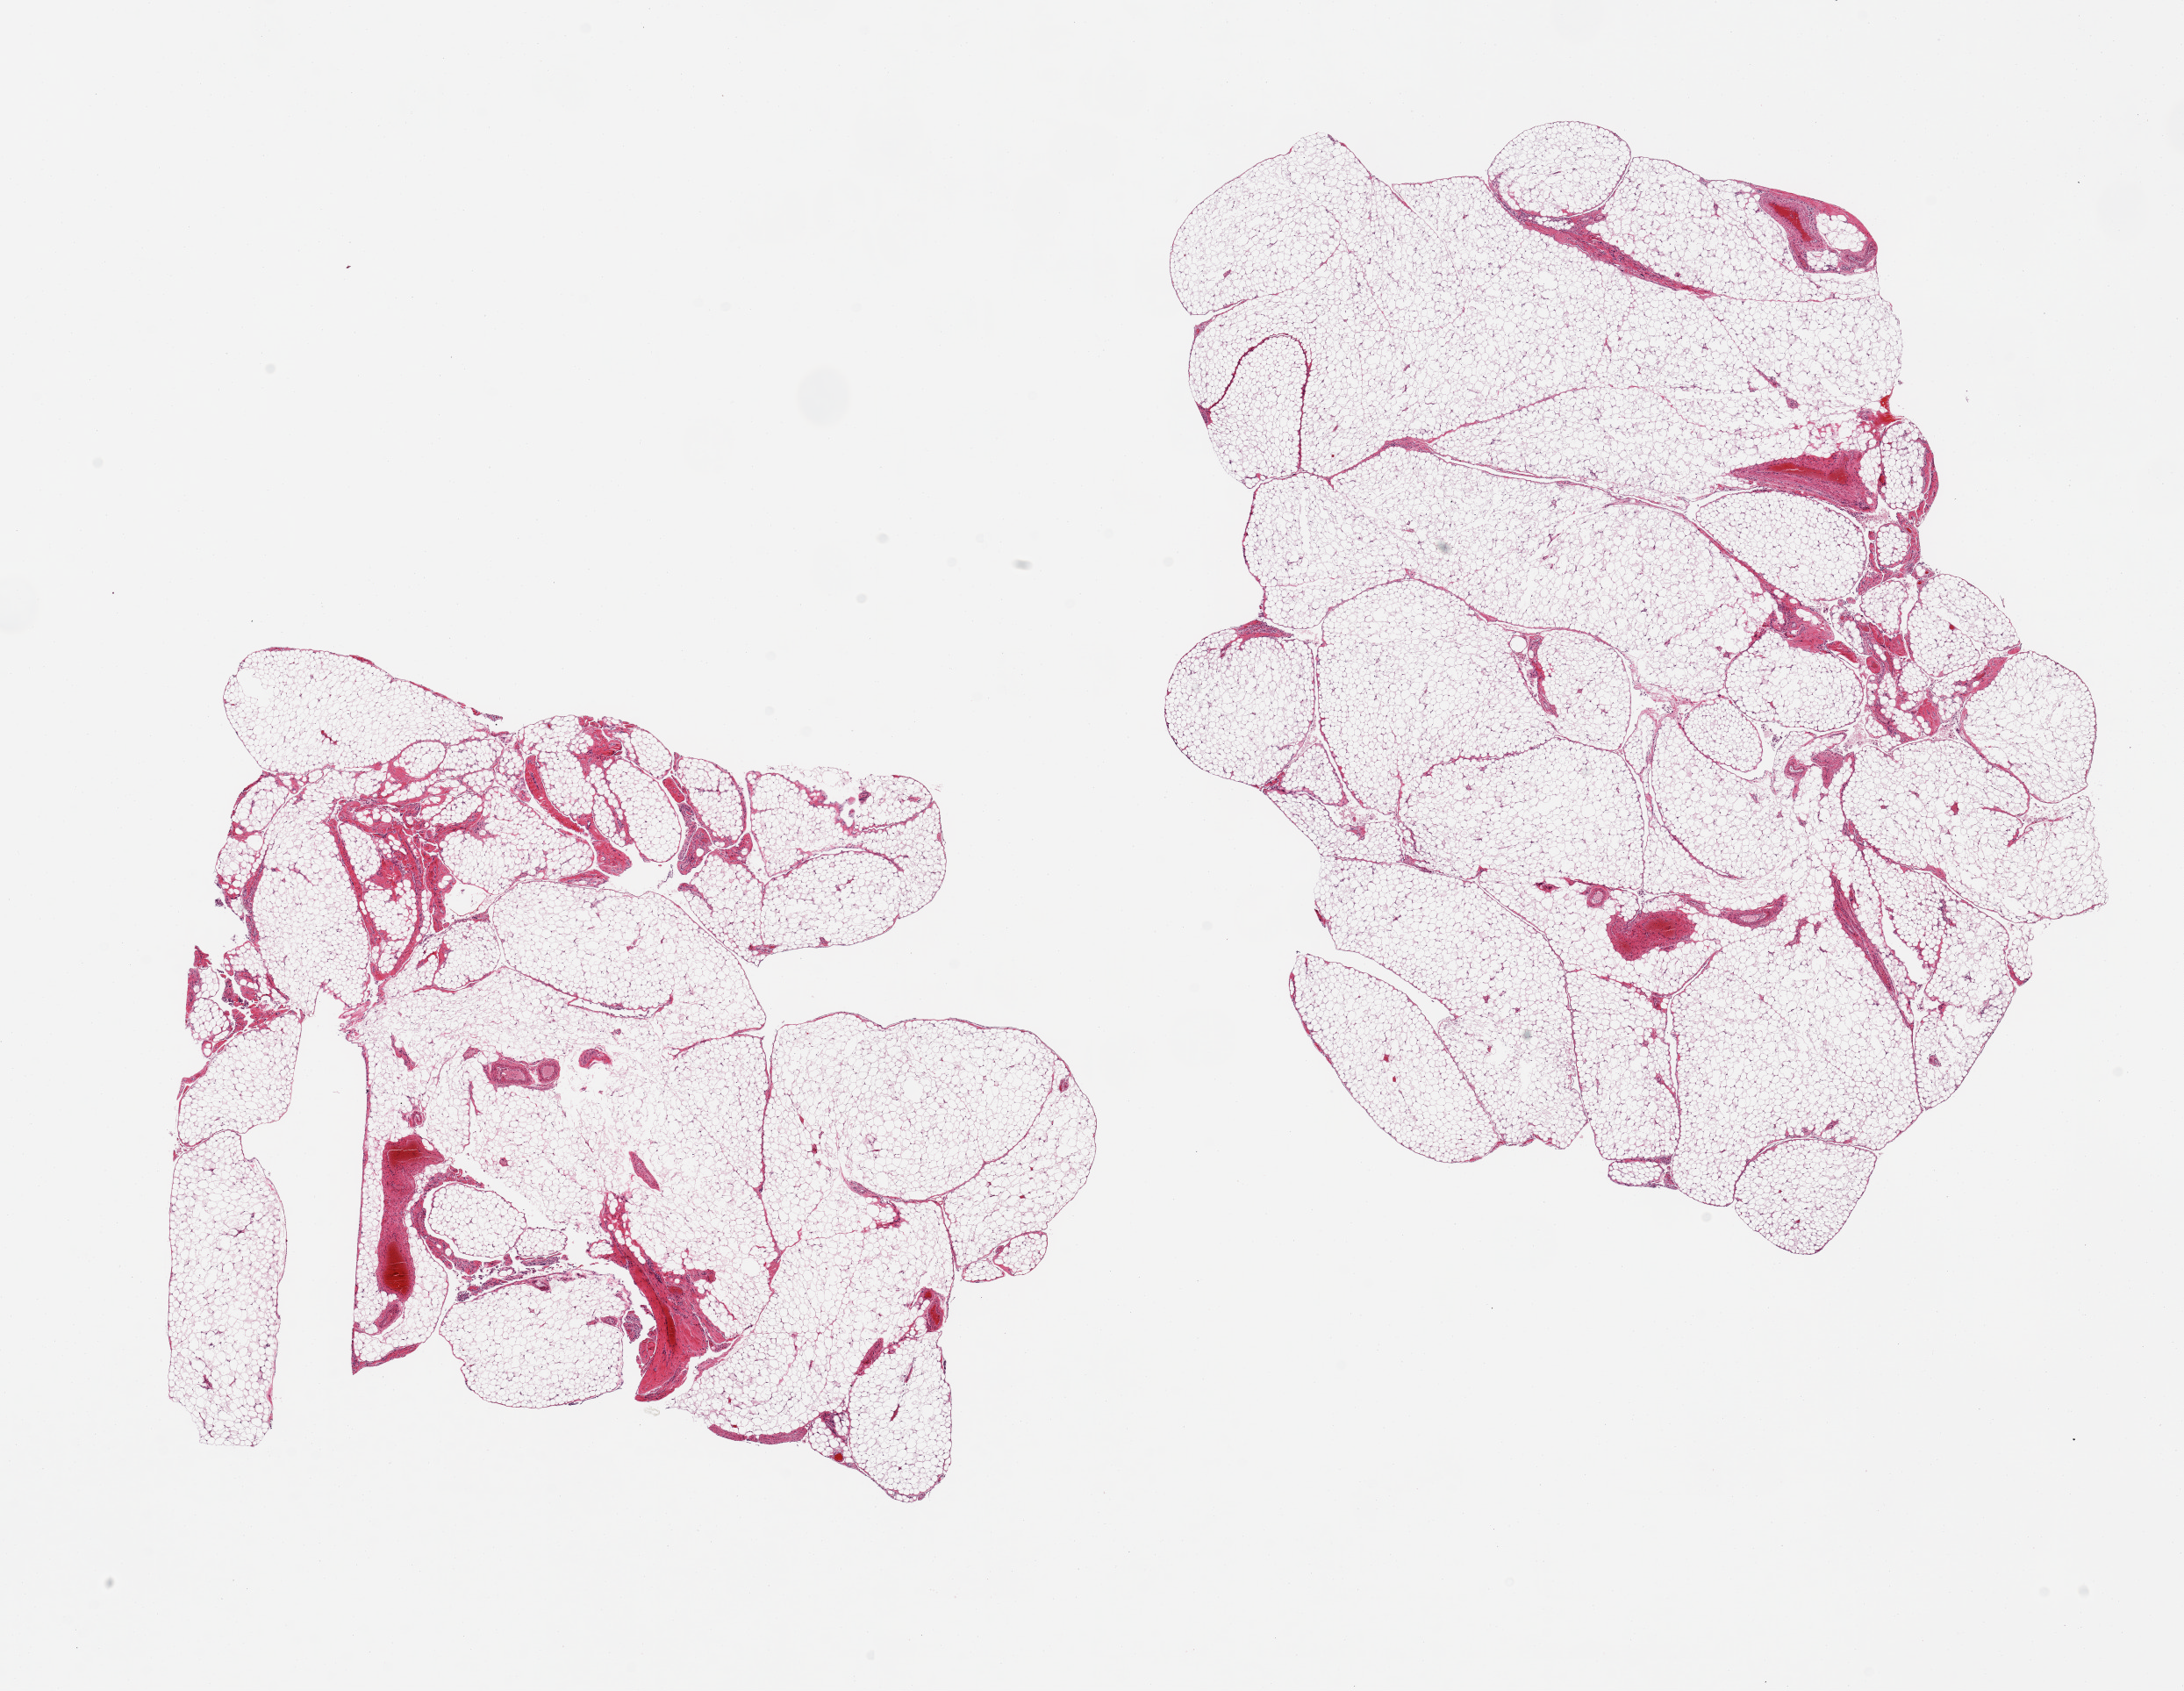
Whole-slide image, hematoxylin and eosin (H&E) stain, a low-resolution overview of the entire scanned area, about 19.7 x 15.2 mm (acquisition: 20x scan), PAXgene-fixed, paraffin-embedded tissue, sampled site (target tissue): omentum, tissue donor sample.
- reviewer comment on this tissue sample: 2 pieces, ~10% vascular elements/fascia